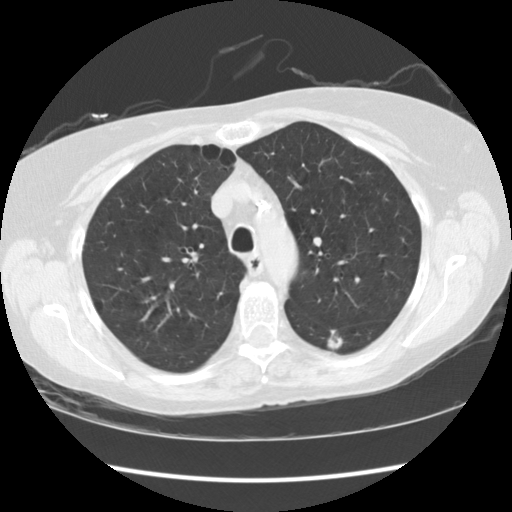
Low-dose screening chest CT, one axial slice. Slice 88 of 119 in the series (ordered by position). Reconstruction kernel STANDARD. 120 kVp. Lung window (W 1500 / L -600 HU). 512 × 512 image matrix, field of view 334 × 334 mm.
Annotated regions visible in this slice (manually delineated by an expert):
- lesion 1 (tumor, lower lobe of left lung): bounding box [x1, y1, x2, y2] px = [327, 330, 343, 348]